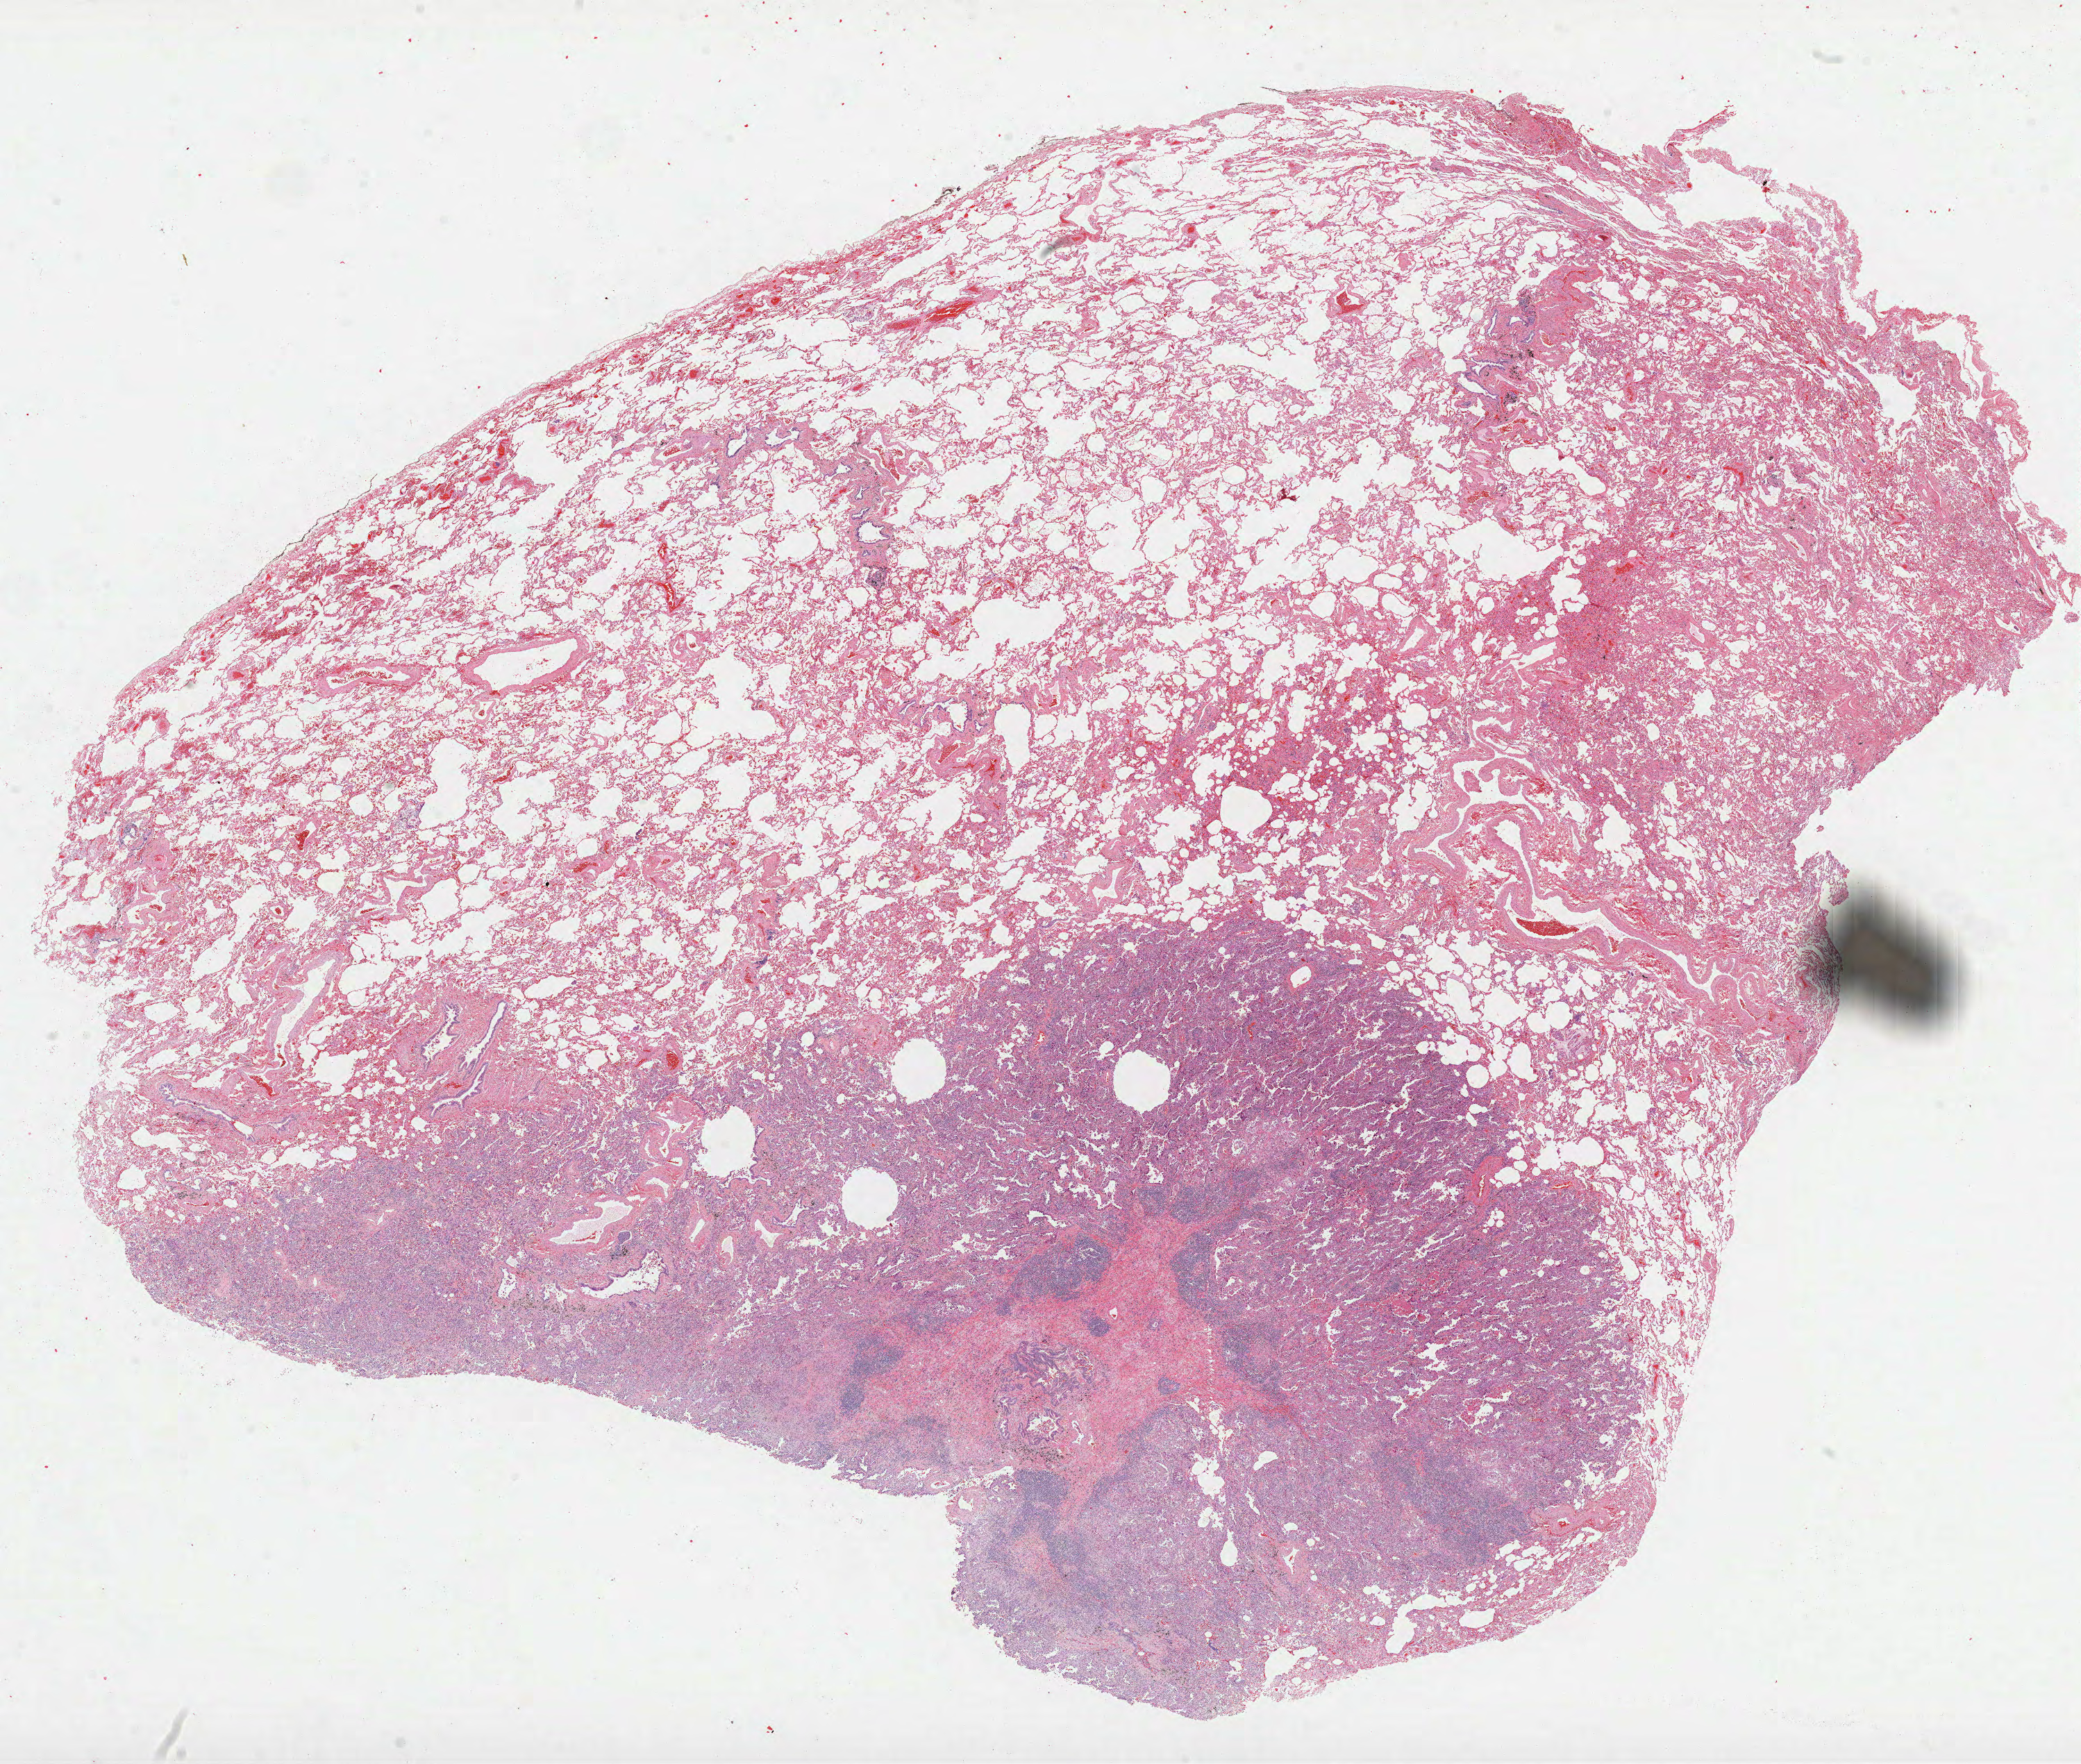
Hematoxylin and eosin (H&E) stained whole-slide image, a low-resolution overview of the entire scanned area, about 24.2 x 20.5 mm. FFPE section. Lung, primary tumour sample. Patient: female, age at initial diagnosis 65 years.
• AJCC pathologic stage: IA (6th edition)
• histologic diagnosis: Adenocarcinoma, NOS (upper lobe, lung)
• laterality: left